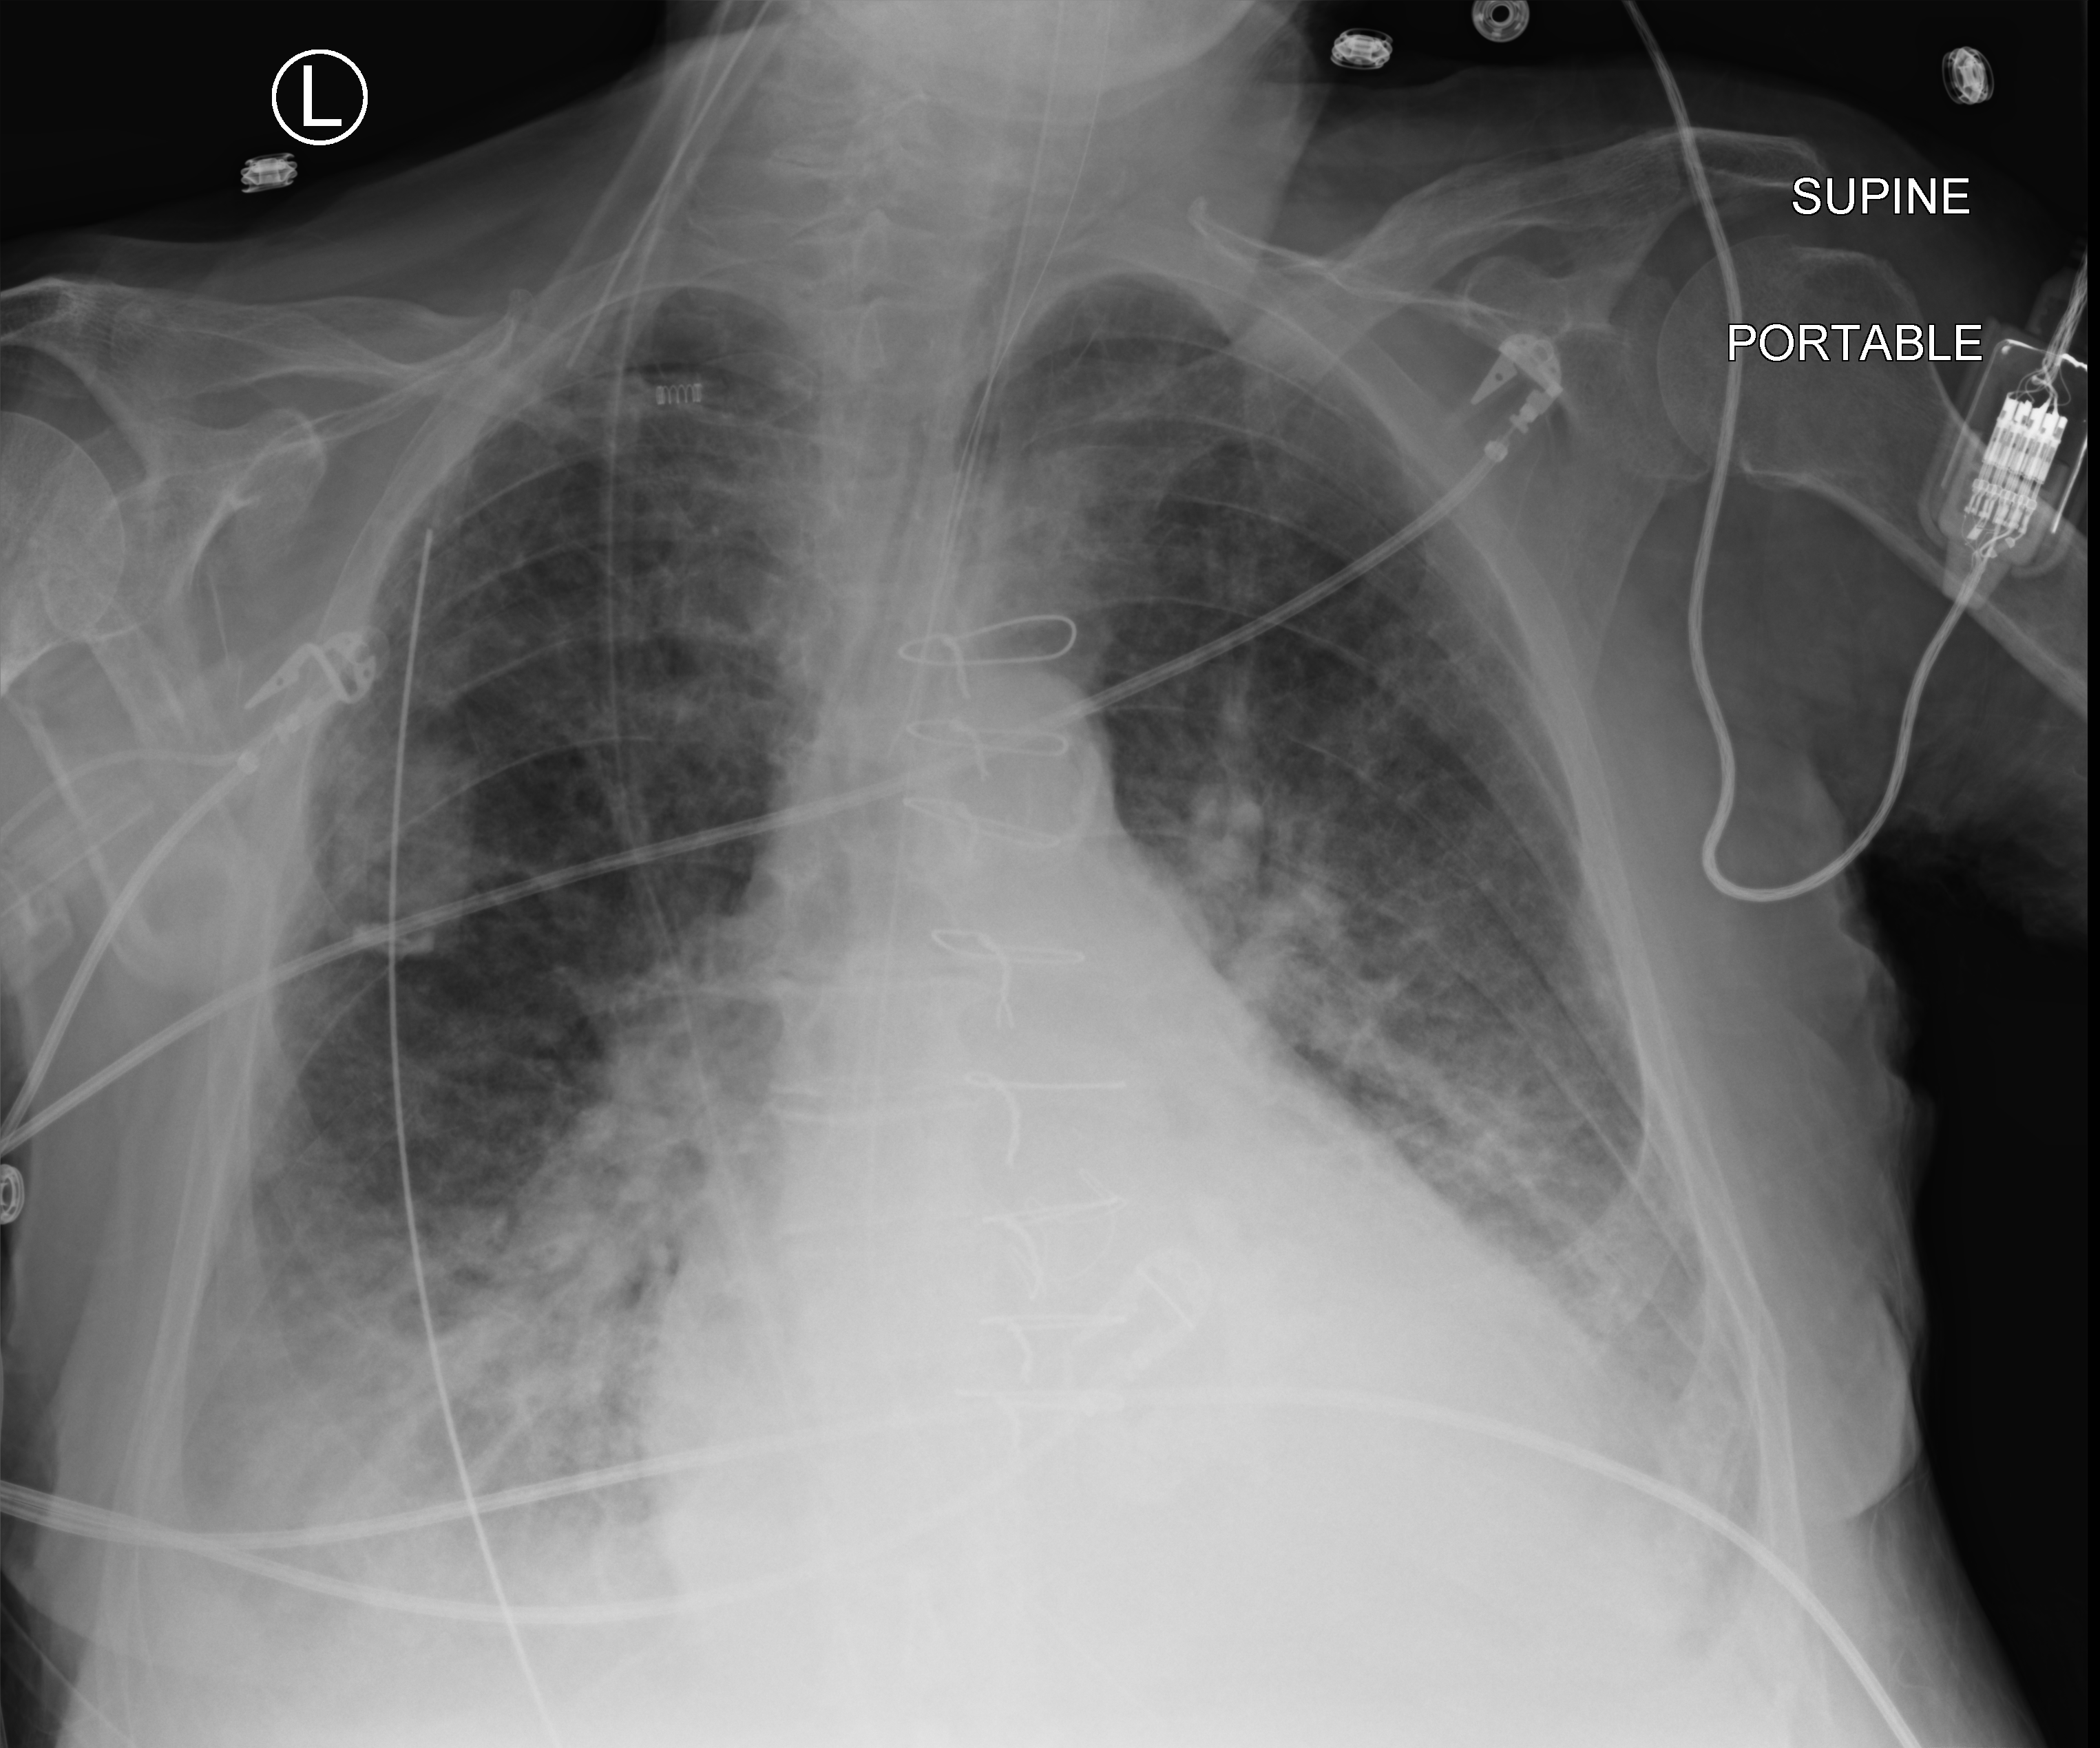
Bedside chest radiograph (computed radiography), anteroposterior (AP) projection. Patient hospitalised with COVID-19; male, aged 75–90 years.
From the hospital-stay record, not from the radiograph (when in the stay this image was taken is not recorded): admitted to intensive care during this hospital stay: yes; length of hospital stay: 40 days.